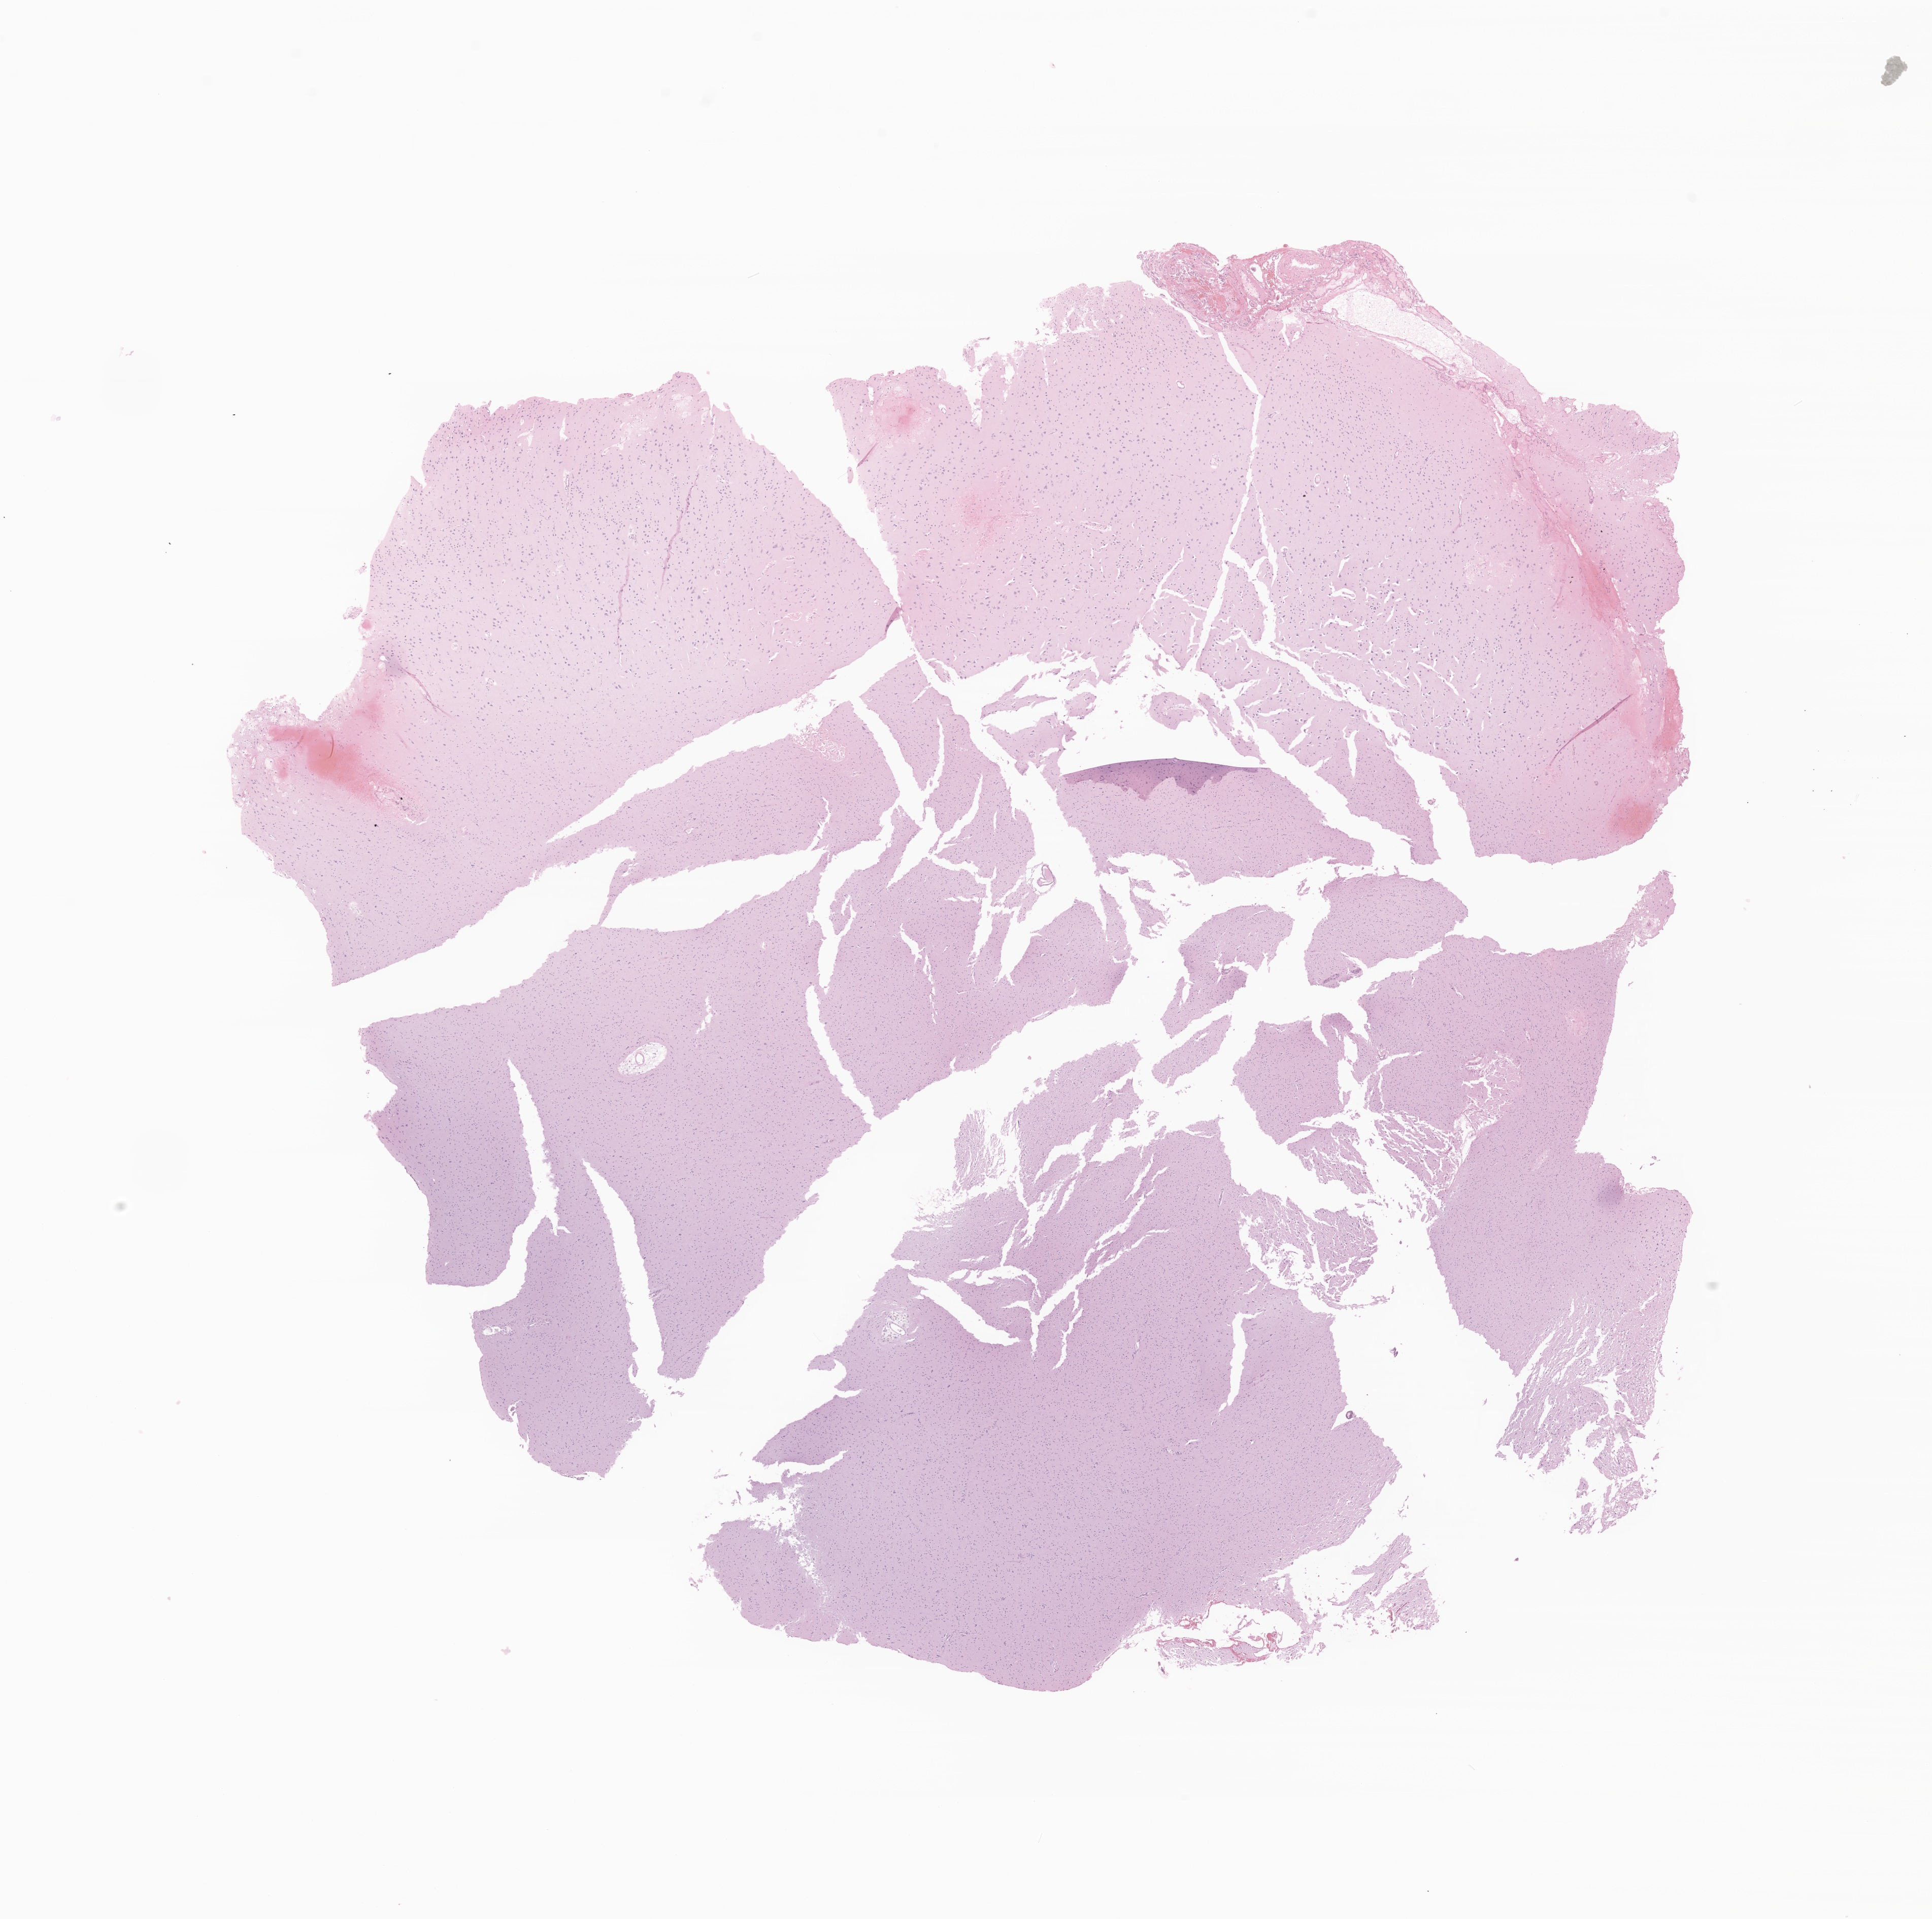
H&E whole-slide image of tumor tissue from the brain, shown as a low-resolution overview of the whole scanned area (about 16.0 x 15.9 mm); FFPE section. Patient: male, age 166 months (13 years 10 months).
Diagnosis: Neoplasm, uncertain whether benign or malignant.